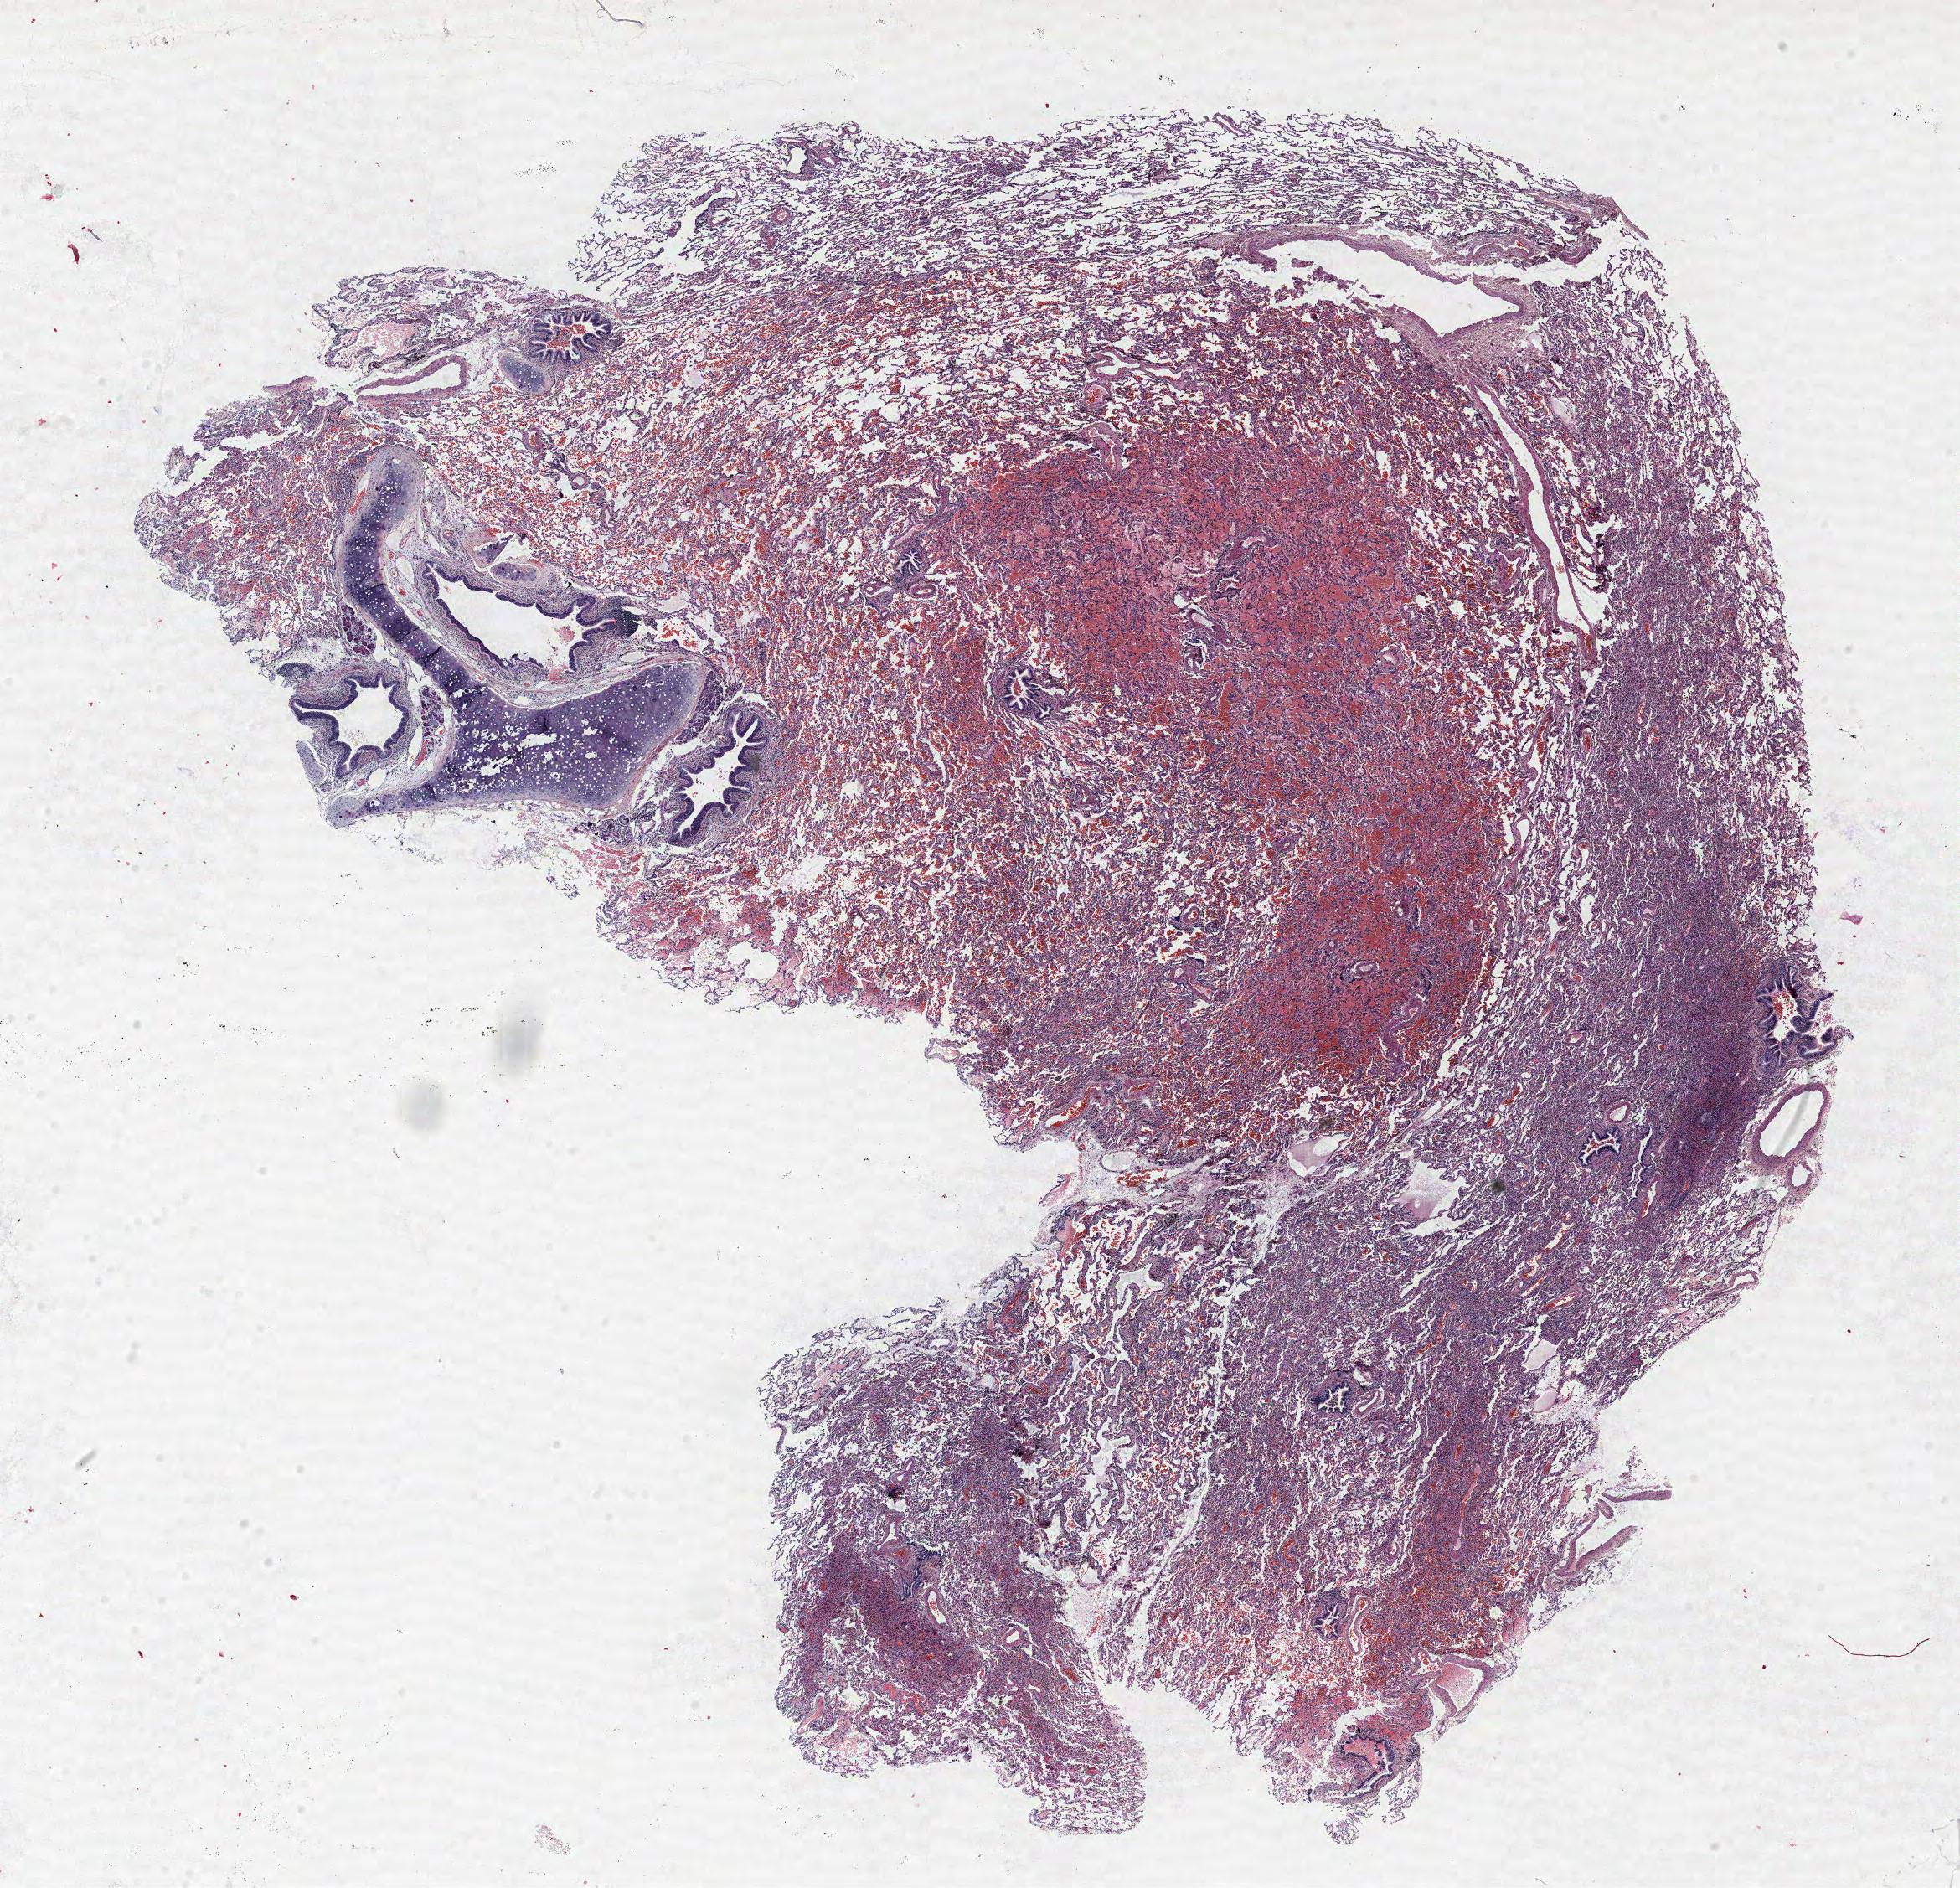
H&E whole-slide image, whole scanned area (about 18.7 x 18.0 mm, acquisition: 40x scan) shown as a low-resolution overview, formalin-fixed paraffin-embedded (FFPE) section, lung tissue. Male, age 57 at enrolment. Current smoker at enrolment. Grade: poorly differentiated (G3).
Stage (AJCC 6th edition): IA. Tumour size (pathology): 24 mm. Participant's lung-cancer diagnosis: Adenocarcinoma, NOS. Primary tumour location (clinical record): right lower lobe.